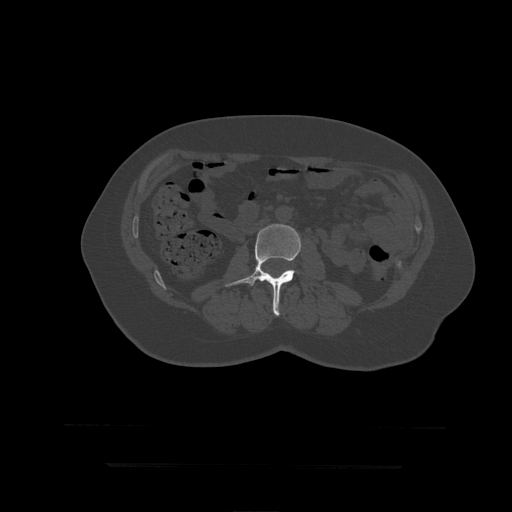
CT including the spine, one axial slice; position 123 of 399 along the scan axis; reconstruction kernel STANDARD; bone window (W 1800 / L 400 HU); 1.25 mm slice thickness; 512 × 512 image matrix, field of view 450 × 450 mm. Patient age 41 years. Case-level facts recorded for this patient, not image findings: primary cancer: breast.
Annotated regions visible in this slice (semi-automatically segmented with operator editing):
- L3 vertebra: box from (x=225, y=224) to (x=301, y=316) px